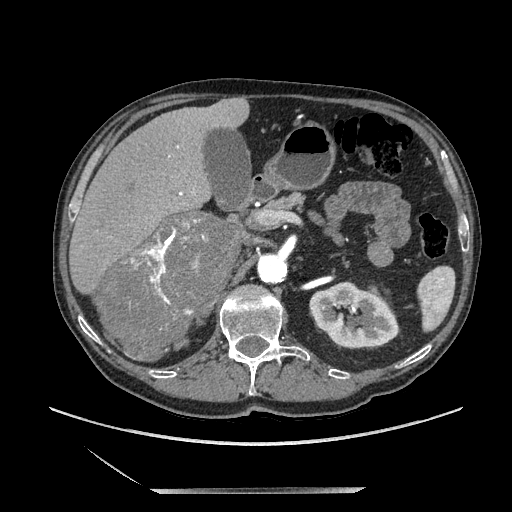
Contrast-enhanced abdominal CT, one axial slice. Position 121 of 243 along the scan axis. Soft-tissue window (W 400 / L 40 HU). 512 × 512 image matrix, field of view 420 × 420 mm. Male patient. From the clinical record (not read from this slice): diagnosis: adrenocortical carcinoma; tumour side: right adrenal; tumour size at pathology: 16 cm; Ki-67 index: 17 %; stage (as recorded): 3.
Annotated regions visible in this slice (semi-automatically segmented with operator editing):
- mass: bounding box (x1, y1, x2, y2) in pixels: (97, 214, 236, 358)